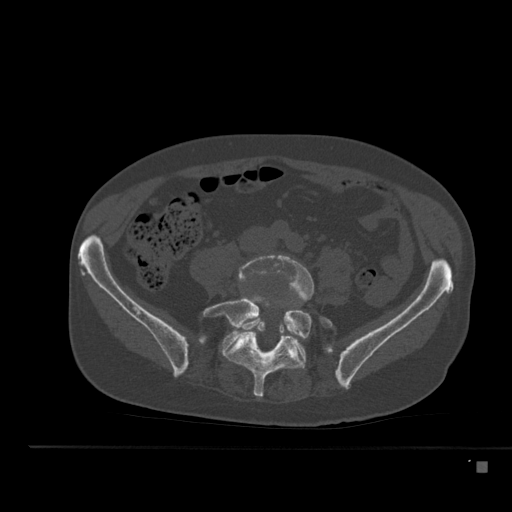
CT including the spine, one axial slice. Position 129 of 517 along the scan axis. 120 kVp. Bone window (W 1800 / L 400 HU). 1.5 mm slice thickness. 512 × 512 image matrix. Patient: male, 70 years. From the clinical record (not read from this slice): primary cancer: renal; vertebrae with lytic lesions (as recorded): T4, T6, T10, T12, L3, L4, L5.
Outlined on this slice (semi-automatically segmented with operator editing):
- L4 vertebra: bounding box <238,254,314,338> (left, top, right, bottom; pixels)
- L5 vertebra: <203,292,332,398>